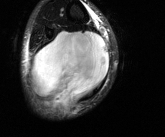
MRI of an extremity soft-tissue mass, one axial slice; slice 43 of 81 in the series (ordered by position); T2-weighted fat-saturated; MR volume resampled by the dataset authors to the PET/CT grid (not the native acquisition matrix); 3.27 mm slice thickness; 165 × 137 image matrix, field of view 161 × 134 mm. Male patient. Case-level facts recorded for this patient, not image findings: histological type: liposarcoma - round cell; grade: high; site of the primary tumour: right calf.
Outlined on this slice (expert contour drawn on MRI and transferred to this co-registered scan by the dataset authors):
- gross tumour volume (mass): box from (x=32, y=30) to (x=109, y=113) px